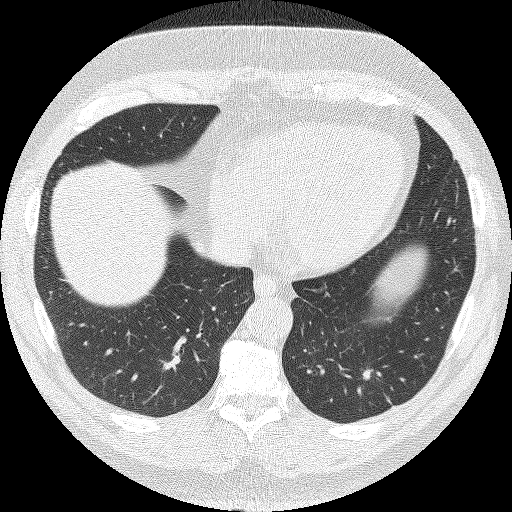
Low-dose screening chest CT, axial slice; baseline screening round; lung window (W 1500 / L -600 HU); 2 mm slice thickness; lung (sharp) reconstruction kernel (FC51); 120 kVp; 512 × 512 image matrix. Male participant, aged 62 years at enrolment. Current smoker at enrolment.
- Lesion marked by an expert reader, bounding box [x1, y1, x2, y2] px = [348, 350, 407, 398].
- The screening reader recorded 2 non-calcified nodules or masses ≥4 mm on this exam; which of them this box marks is not recorded.
- Official screen result: positive, change unspecified: nodule(s) >= 4 mm or enlarging nodule(s), mass(es), or other non-specific abnormalities suspicious for lung cancer.